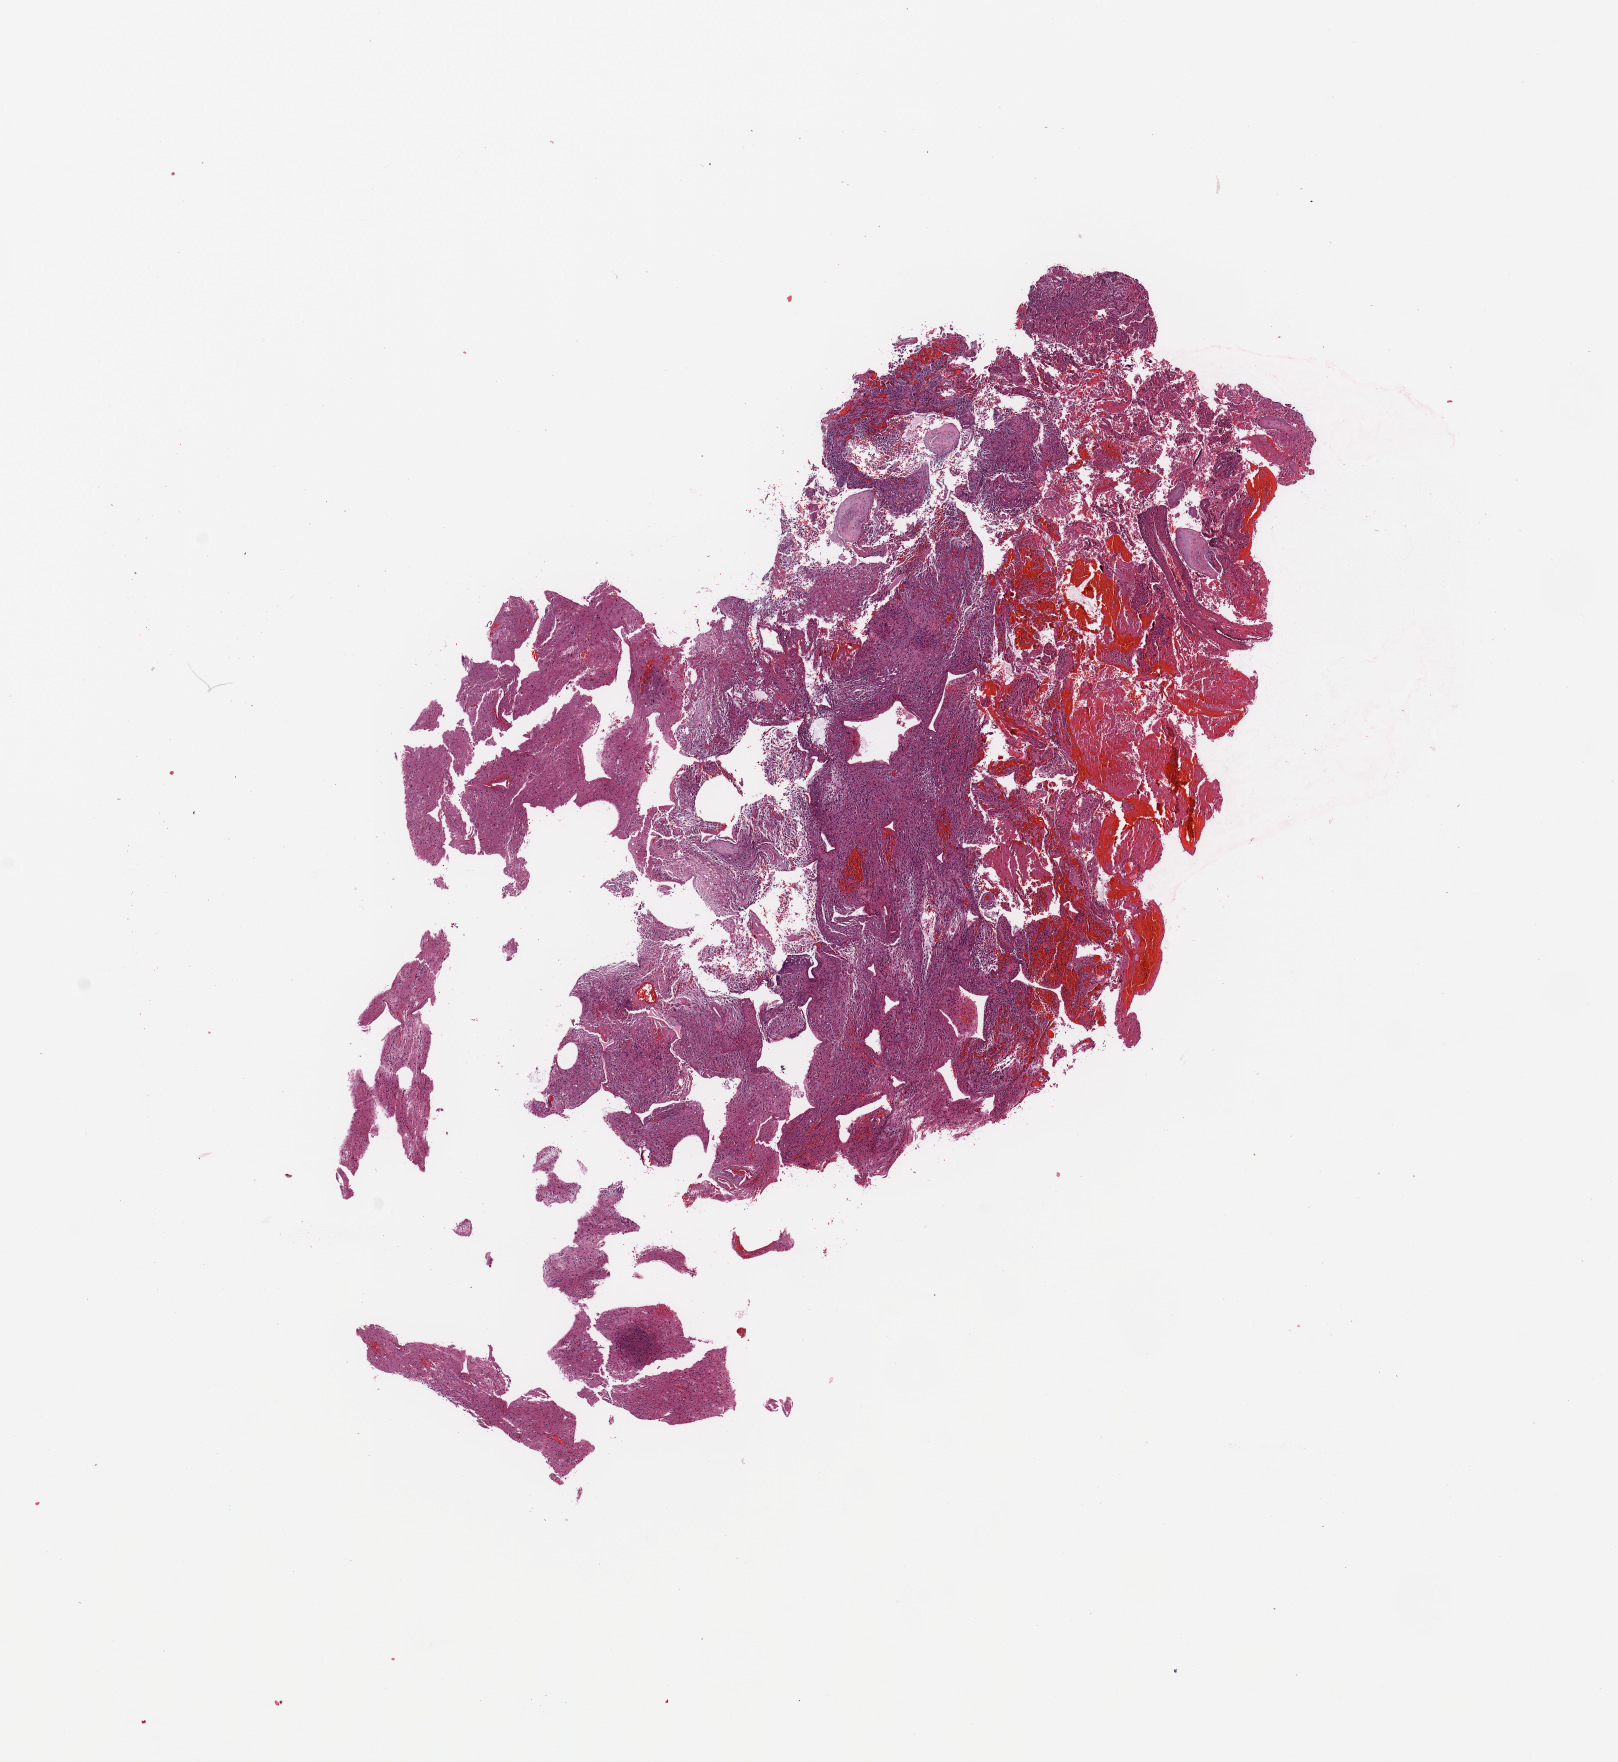
Whole-slide histology image, Hematoxylin and eosin (H&E) stained — whole scanned area (about 12.8 x 13.9 mm, acquisition: 20x scan) shown as a low-resolution overview. Tumour tissue sample, sampled site: frontal lobe. Male, 45 y/o. Slide review estimates, as recorded: tumour nuclei 70%, necrosis 10%.
- diagnosis: Glioblastoma
- primary tumour site (as recorded): frontal lobe